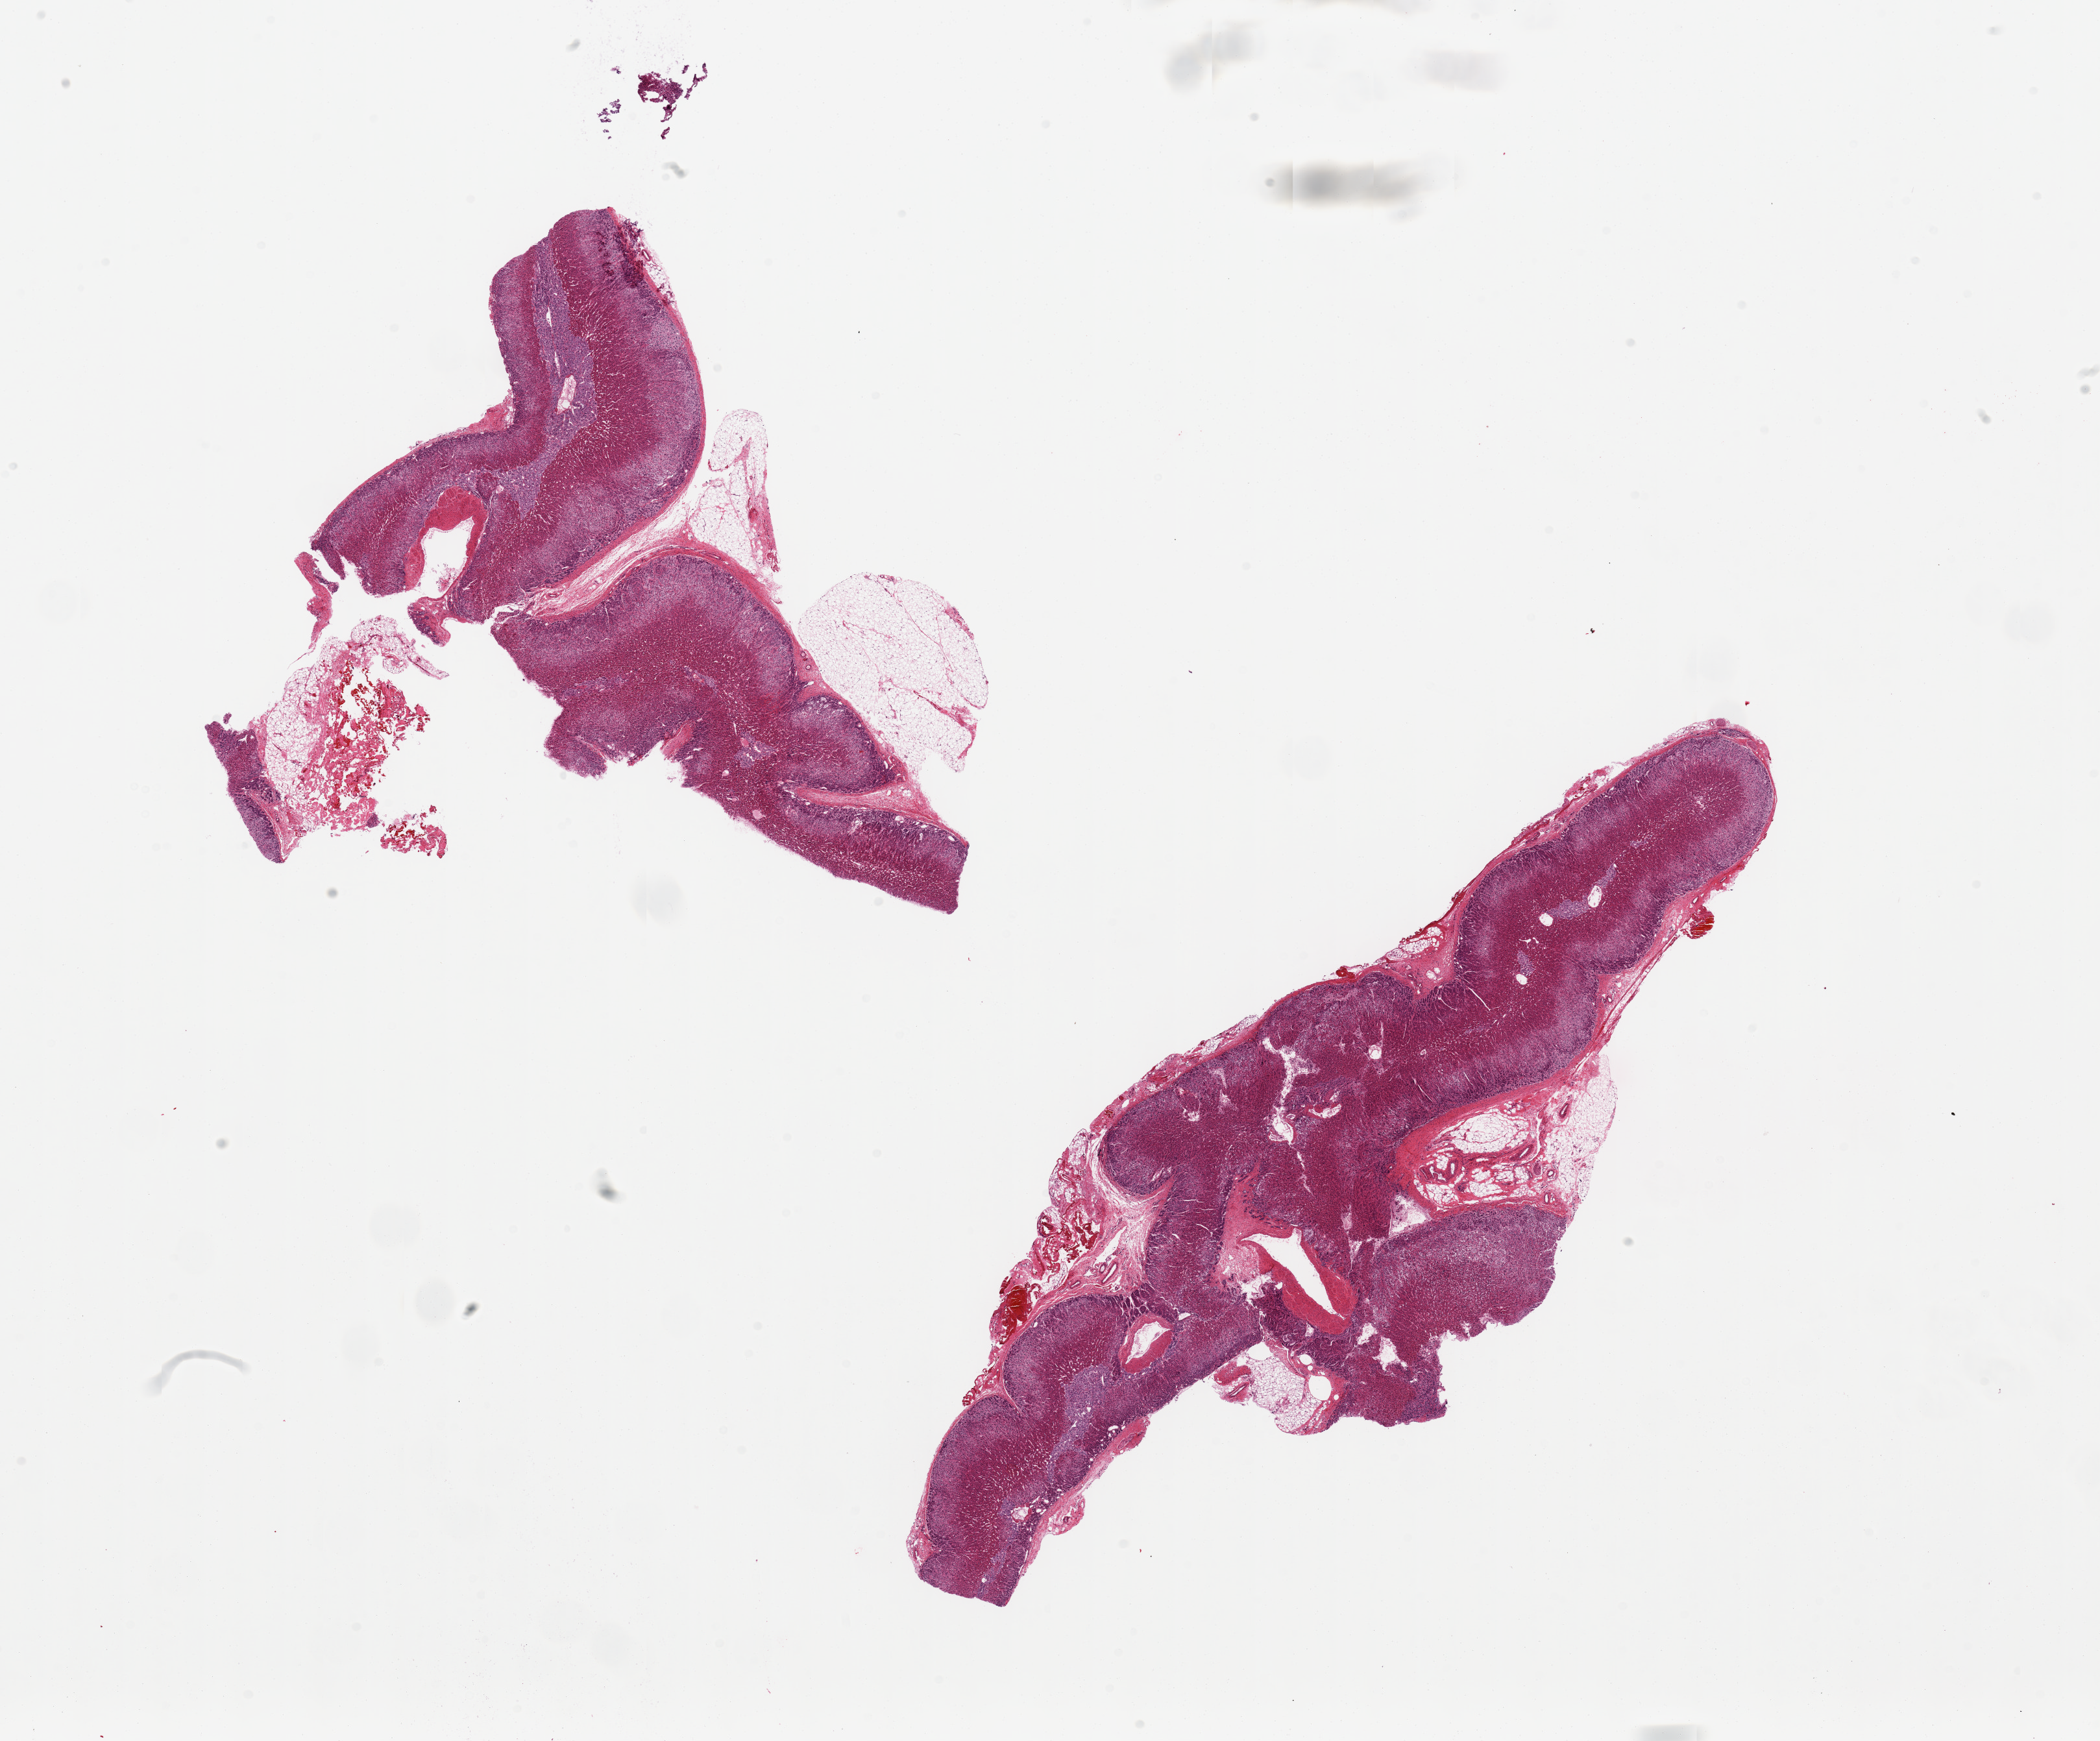
Digitized haematoxylin and eosin-stained section, a low-resolution overview of the entire scanned area, about 25.6 x 21.2 mm (from a 20x scan); PAXgene-fixed paraffin-embedded (PFPE) section; sampled site (target tissue): adrenal gland; tissue donor sample. Donor: female.
- reviewer comment on this tissue sample: 2 pieces, includes 10-20% attached fat/ vessels